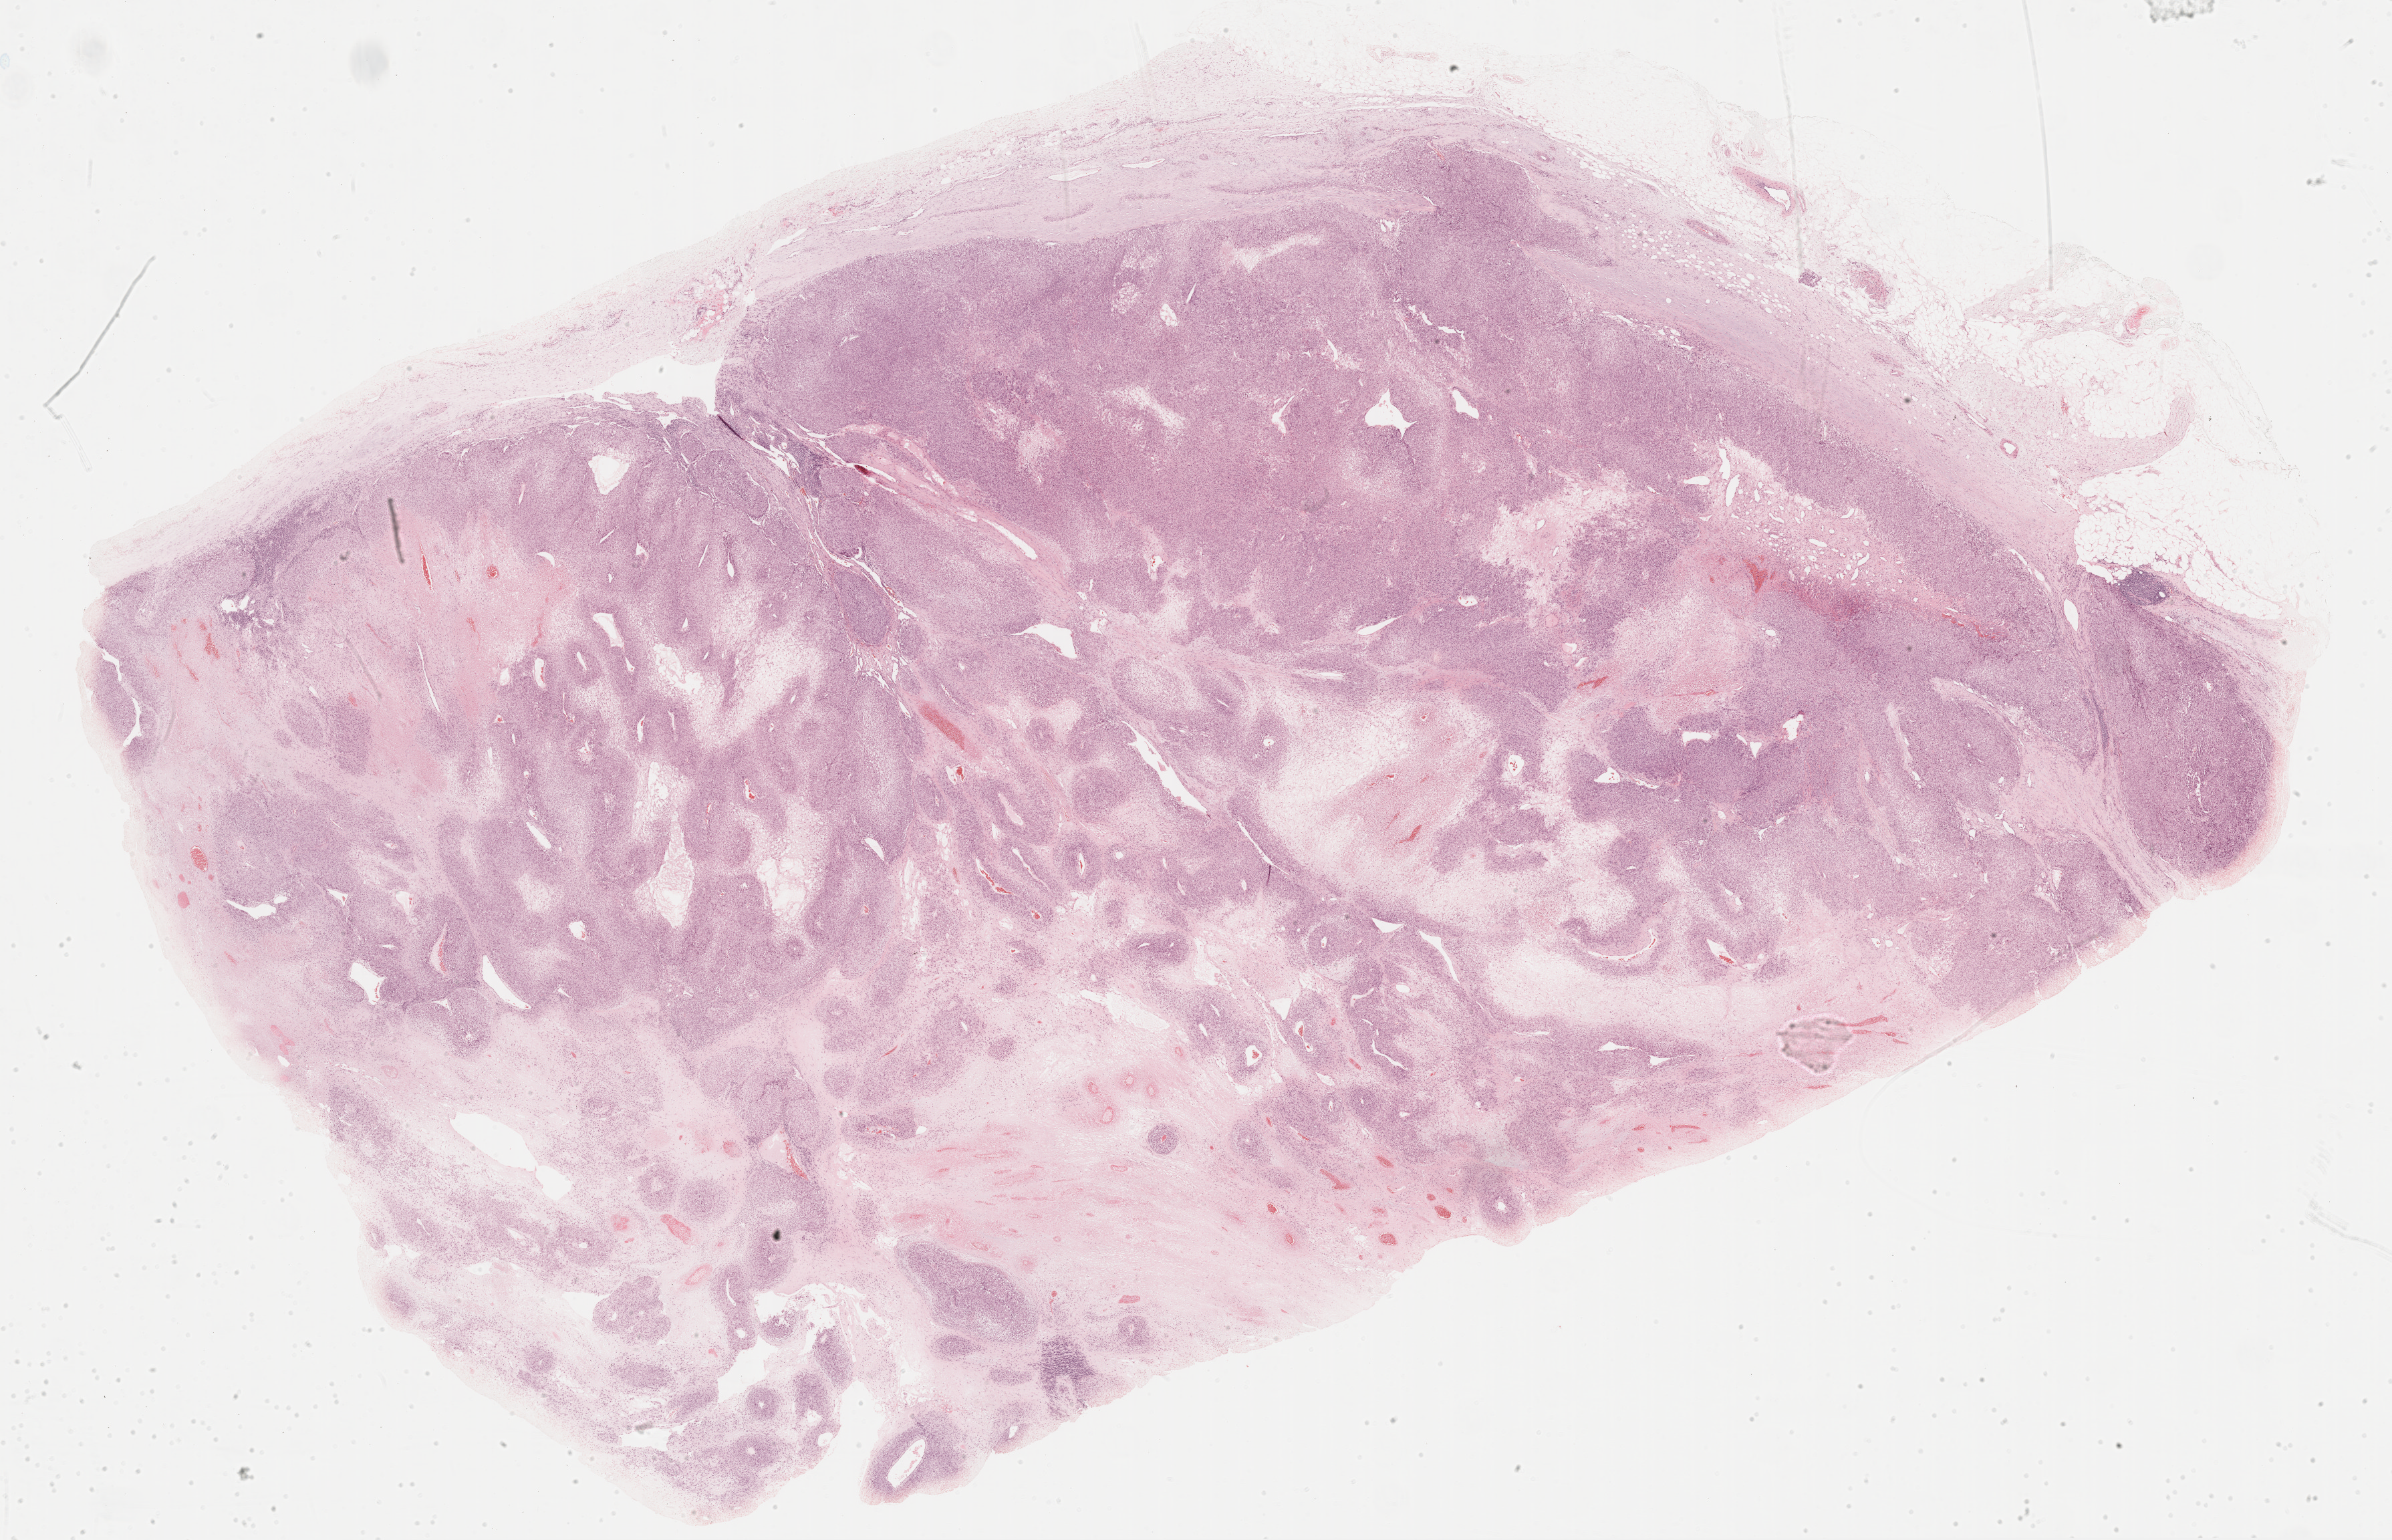
Digitized H&E-stained tissue section (whole slide) — whole scanned area (about 28.9 x 18.6 mm) shown as a low-resolution overview. Formalin-fixed paraffin-embedded (FFPE) diagnostic section. Metastatic tumour sample, sampled site: lymph node. Female patient; age at initial diagnosis 53 years.
* this section: metastatic tumour tissue
* patient diagnosis: Malignant melanoma, NOS